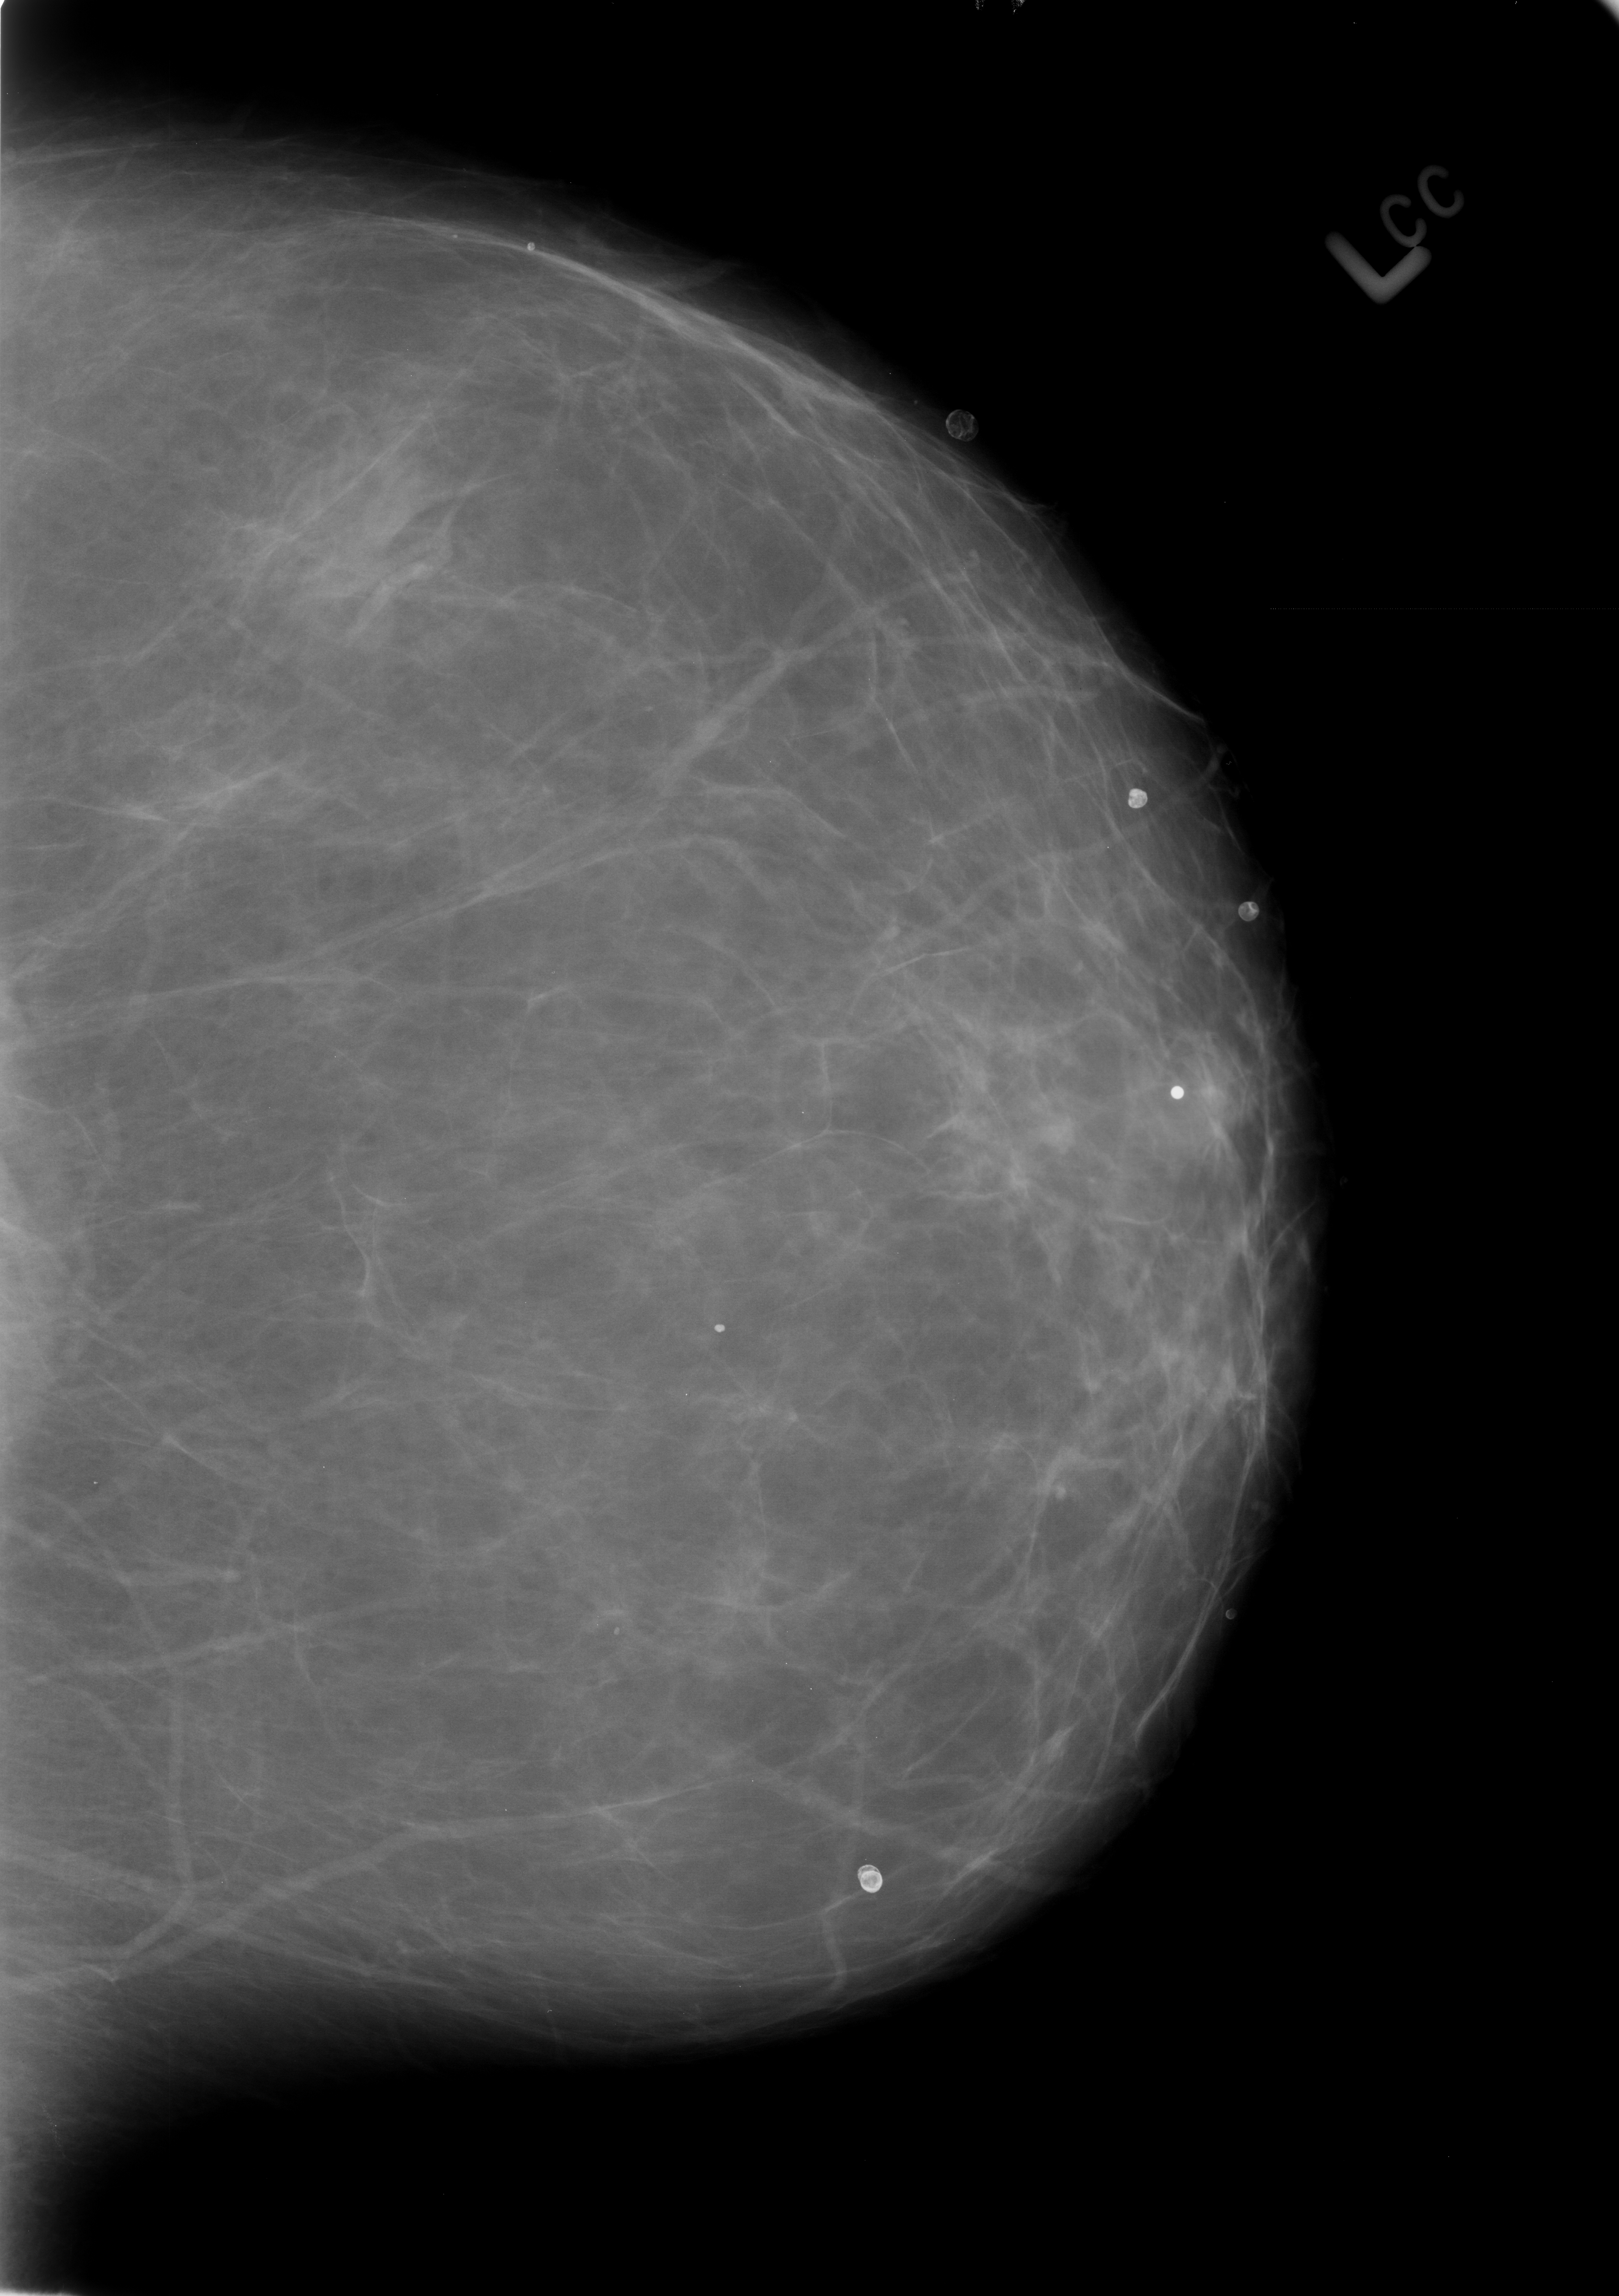
Scanned film-screen mammogram. Left breast. Craniocaudal (CC) view. Breast composition: almost entirely fatty (BI-RADS density category 1 of 4). 1619 × 2296 image matrix.
Expert-marked regions of interest on this film, with their recorded descriptors:
- Finding 1 of 5: calcifications, morphology lucent center; BI-RADS assessment category 2; subtlety rating 5 on a 1 (subtle) to 5 (obvious) scale; benign; no additional work-up was recommended (outcome (as recorded, no biopsy): benign without callback): bounding box [x1, y1, x2, y2] px = [706, 1315, 734, 1343]
- Finding 2 of 5: calcifications, morphology lucent center; BI-RADS assessment category 2; subtlety rating 5 on a 1 (subtle) to 5 (obvious) scale; outcome (as recorded, no biopsy): benign without callback (not worked up further): [843, 1840, 903, 1906]
- Finding 3 of 5: calcifications, morphology eggshell; BI-RADS assessment category 2; subtlety rating 5 on a 1 (subtle) to 5 (obvious) scale; benign; no additional work-up was recommended (outcome (as recorded, no biopsy): benign without callback): [941, 403, 988, 447]
- Finding 4 of 5: calcifications, morphology lucent center; BI-RADS assessment category 2; benign; no additional work-up was recommended (outcome (as recorded, no biopsy): benign without callback): [1114, 781, 1154, 815]
- Finding 5 of 5: calcifications, morphology lucent center; BI-RADS assessment category 2; subtlety rating 5 on a 1 (subtle) to 5 (obvious) scale; outcome (as recorded, no biopsy): benign without callback (not worked up further): [1228, 892, 1271, 929]